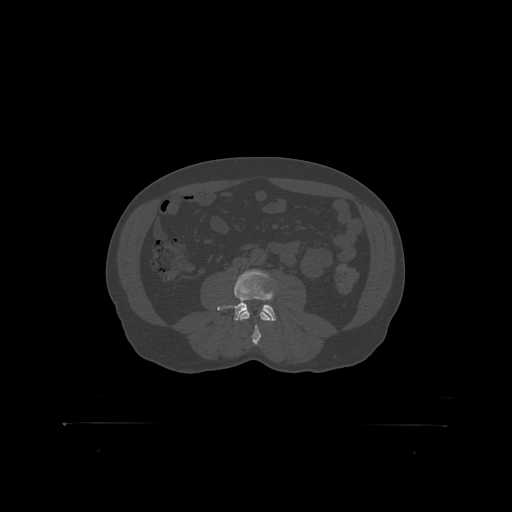
CT including the spine, one axial slice; position 249 of 399 along the scan axis; reconstruction kernel STANDARD; bone window (W 1800 / L 400 HU); 1.25 mm slice thickness; 512 × 512 image matrix, field of view 650 × 650 mm. Male patient, age 46 years. From the clinical record (not read from this slice): primary cancer: skin.
Annotated regions visible in this slice (semi-automatic segmentation, software-assisted and operator-edited):
- L3 vertebra: bounding box [x1, y1, x2, y2] px = [240, 311, 269, 319]
- L4 vertebra: [220, 270, 275, 317]